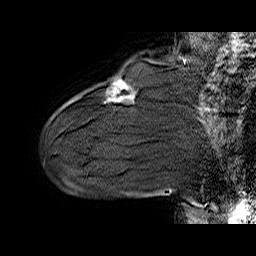
Breast MRI (dynamic contrast-enhanced), one sagittal slice. Position 13 of 60 along the scan axis. Dynamic contrast-enhanced series, time point 2 of 6 at this slice position (early post-contrast). 1.5 T. TE 6.4 ms, TR 32.9 ms. 4 mm slice thickness. 256 × 256 image matrix, field of view 200 × 200 mm. Female patient. From the clinical record (not read from this slice): setting: breast cancer imaged before/during neoadjuvant chemotherapy; receptor status: HER2-positive.
Annotated regions visible in this slice (semi-automatic segmentation, software-assisted and operator-edited):
- analysis volume of interest (the breast-tissue region the enhancement analysis was run in; not a lesion): bounding box <107,77,135,103> (left, top, right, bottom; pixels)
- tumour enhancement mask (voxels above the 100 % enhancement threshold inside the analysis volume of interest): <110,82,124,101>